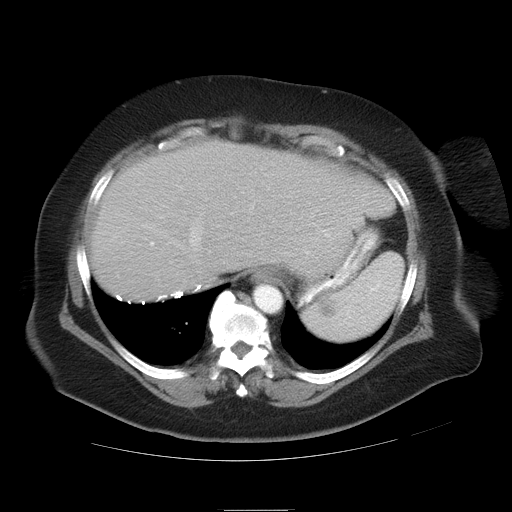
Contrast-enhanced abdominal CT, one axial slice. Slice 30 of 37 in the series (ordered by position). Reconstruction kernel STANDARD. 120 kVp. Intravenous contrast given. Soft-tissue window (W 400 / L 40 HU). 512 × 512 image matrix. Female patient, age 68 years. From the clinical record (not read from this slice): diagnosis: colorectal cancer liver metastases, imaged before liver resection; multiple liver metastases: no; largest metastasis: 2 cm.
Annotated regions visible in this slice (outlined manually by an expert reader):
- hepatic veins: bounding box (x1, y1, x2, y2) in pixels: (156, 172, 276, 264)
- liver: (90, 142, 396, 304)
- planned liver remnant (the part of the liver to remain after resection): (90, 142, 396, 304)
- portal vein (with intrahepatic branches): (150, 241, 154, 246)